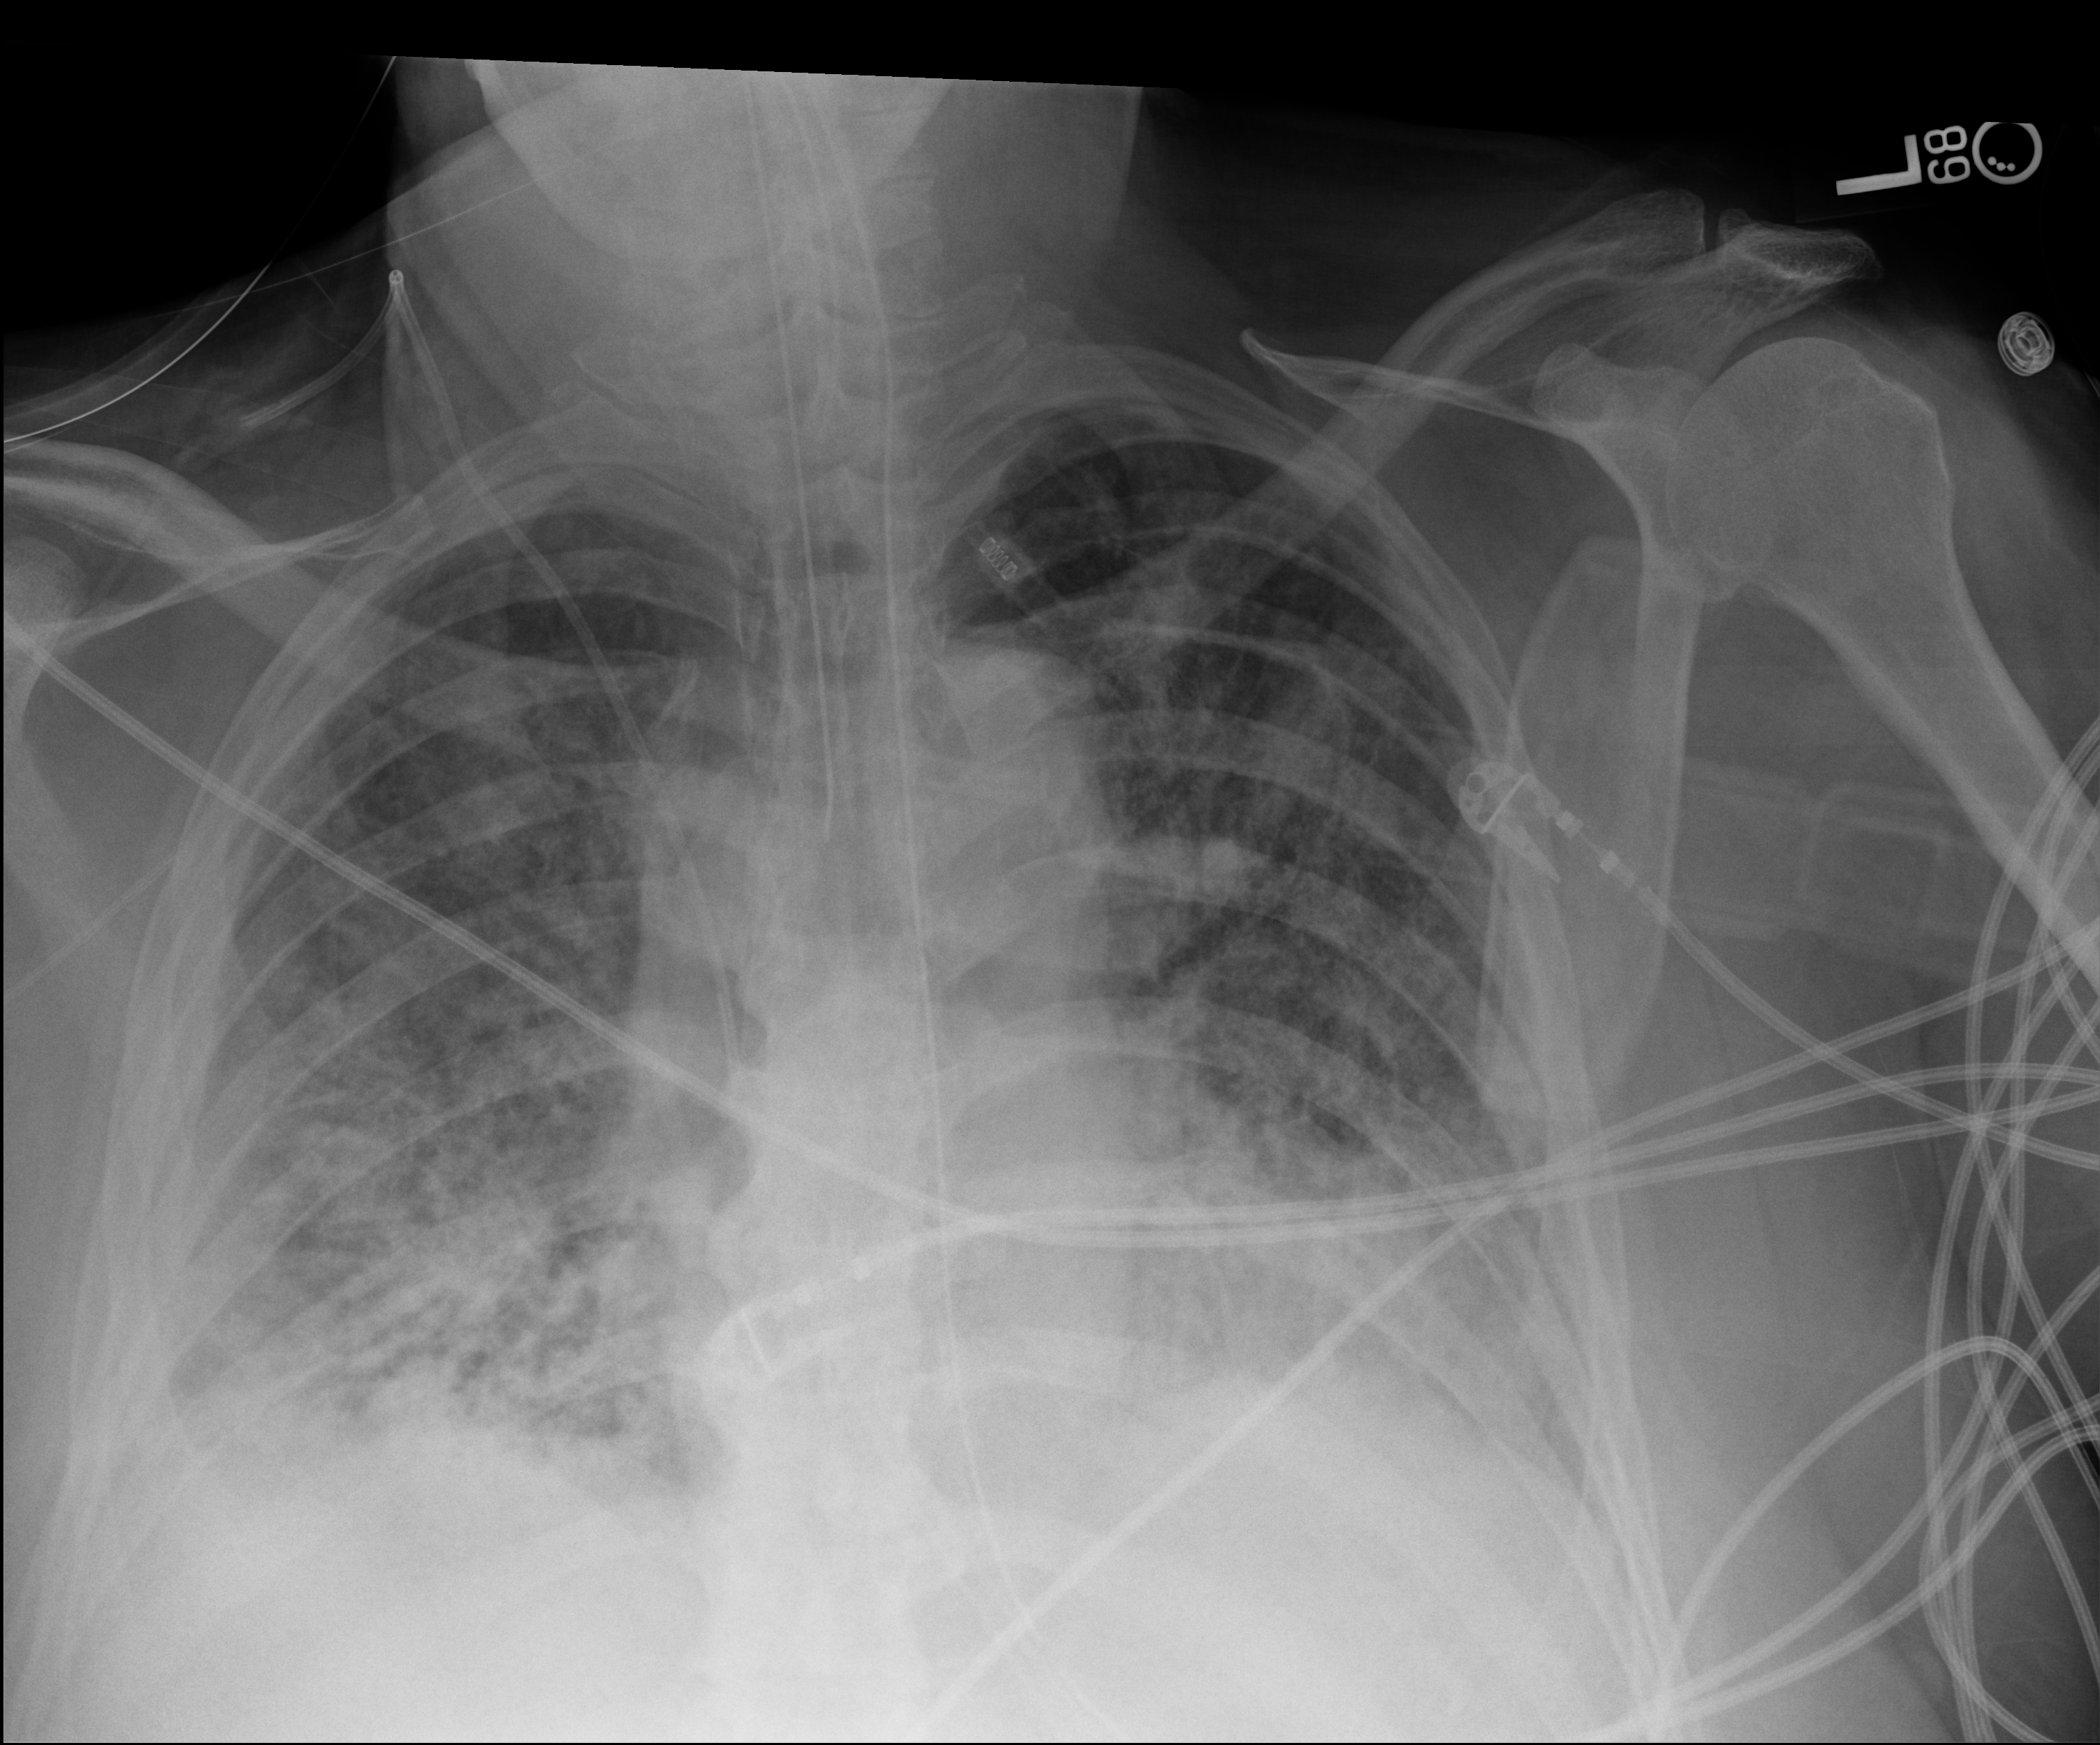
Portable chest radiograph. Patient hospitalised with COVID-19; male, aged 60–74 years.
Hospital-stay facts (about this admission, not read from this image; timing relative to this image not recorded): length of hospital stay: 40 days.